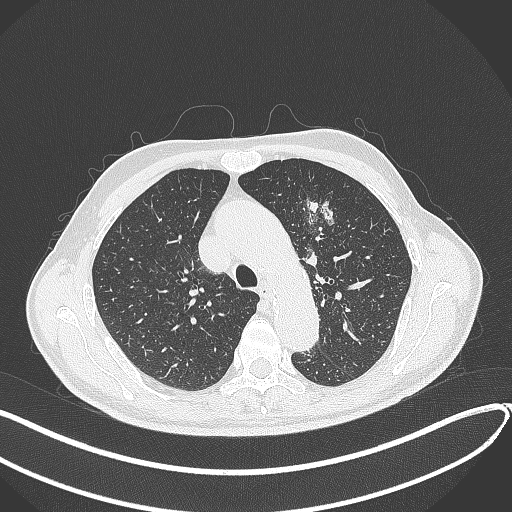
Chest CT, one axial slice; slice 300 of 459 in the series (ordered by position); reconstruction kernel B70f; lung window (W 1500 / L -600 HU); 512 × 512 image matrix, field of view 400 × 400 mm. Patient: male, 74 years. Case-level facts recorded for this patient, not image findings: clinical TNM (as recorded): T2b N0 M1c.
Outlined on this slice (rectangle marked by the reading radiologist):
- lung tumour (recorded histology: adenocarcinoma): box from (x=305, y=196) to (x=340, y=243) px